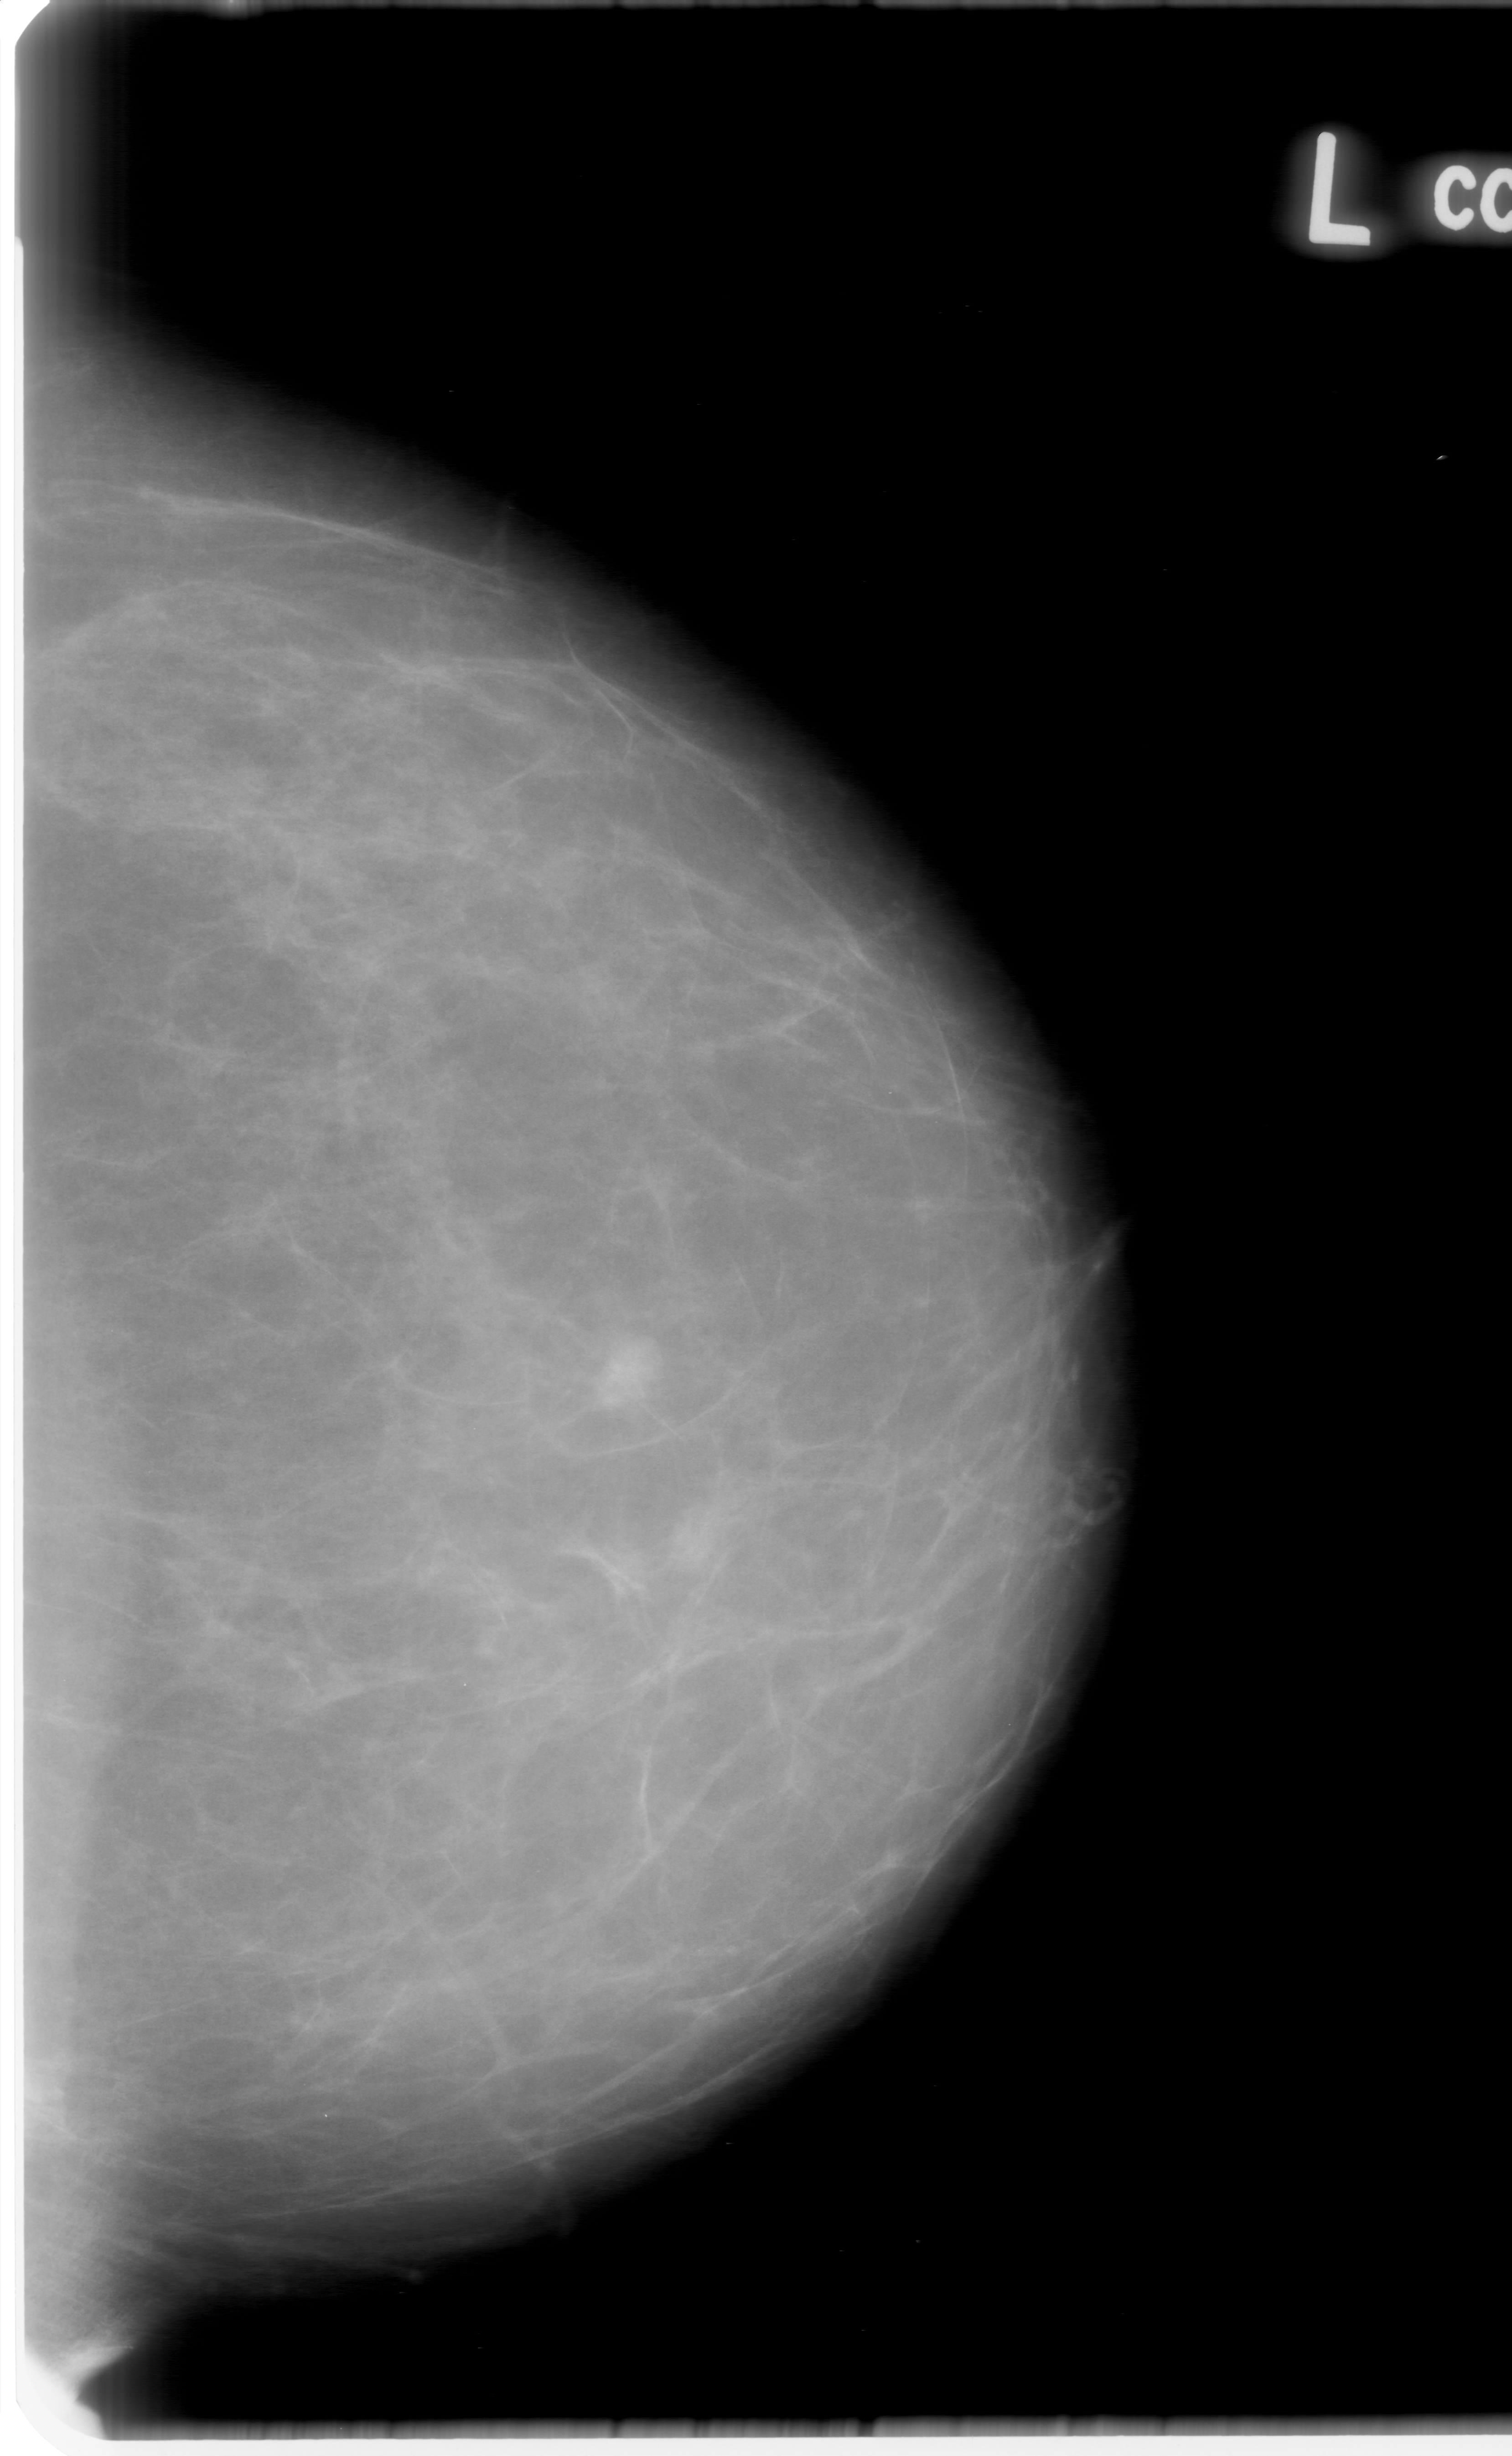
Scanned film-screen mammogram; left breast; CC view; BI-RADS breast density category 1 (scale 1–4).
Finding: mass, shape oval, margins obscured; BI-RADS assessment category 0 (incomplete: needs additional imaging); subtlety rating 5 on a 1 (subtle) to 5 (obvious) scale; pathology result (as recorded, not read from the image): benign.